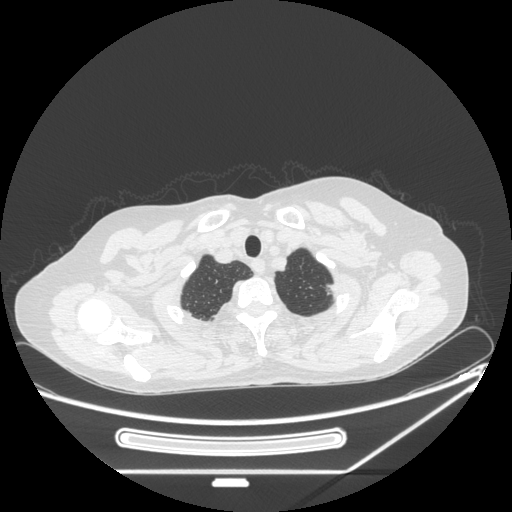
Chest CT, one axial slice; lung window (W 1500 / L -600 HU); 1.25 mm slice thickness; 512 × 512 image matrix. Female patient, age 57 years. Case-level facts recorded for this patient, not image findings: clinical TNM (as recorded): T1c N0 M0.
Outlined on this slice (rectangle marked by the reading radiologist):
- lung tumour (recorded histology: adenocarcinoma): bounding box <321,279,339,300> (left, top, right, bottom; pixels)